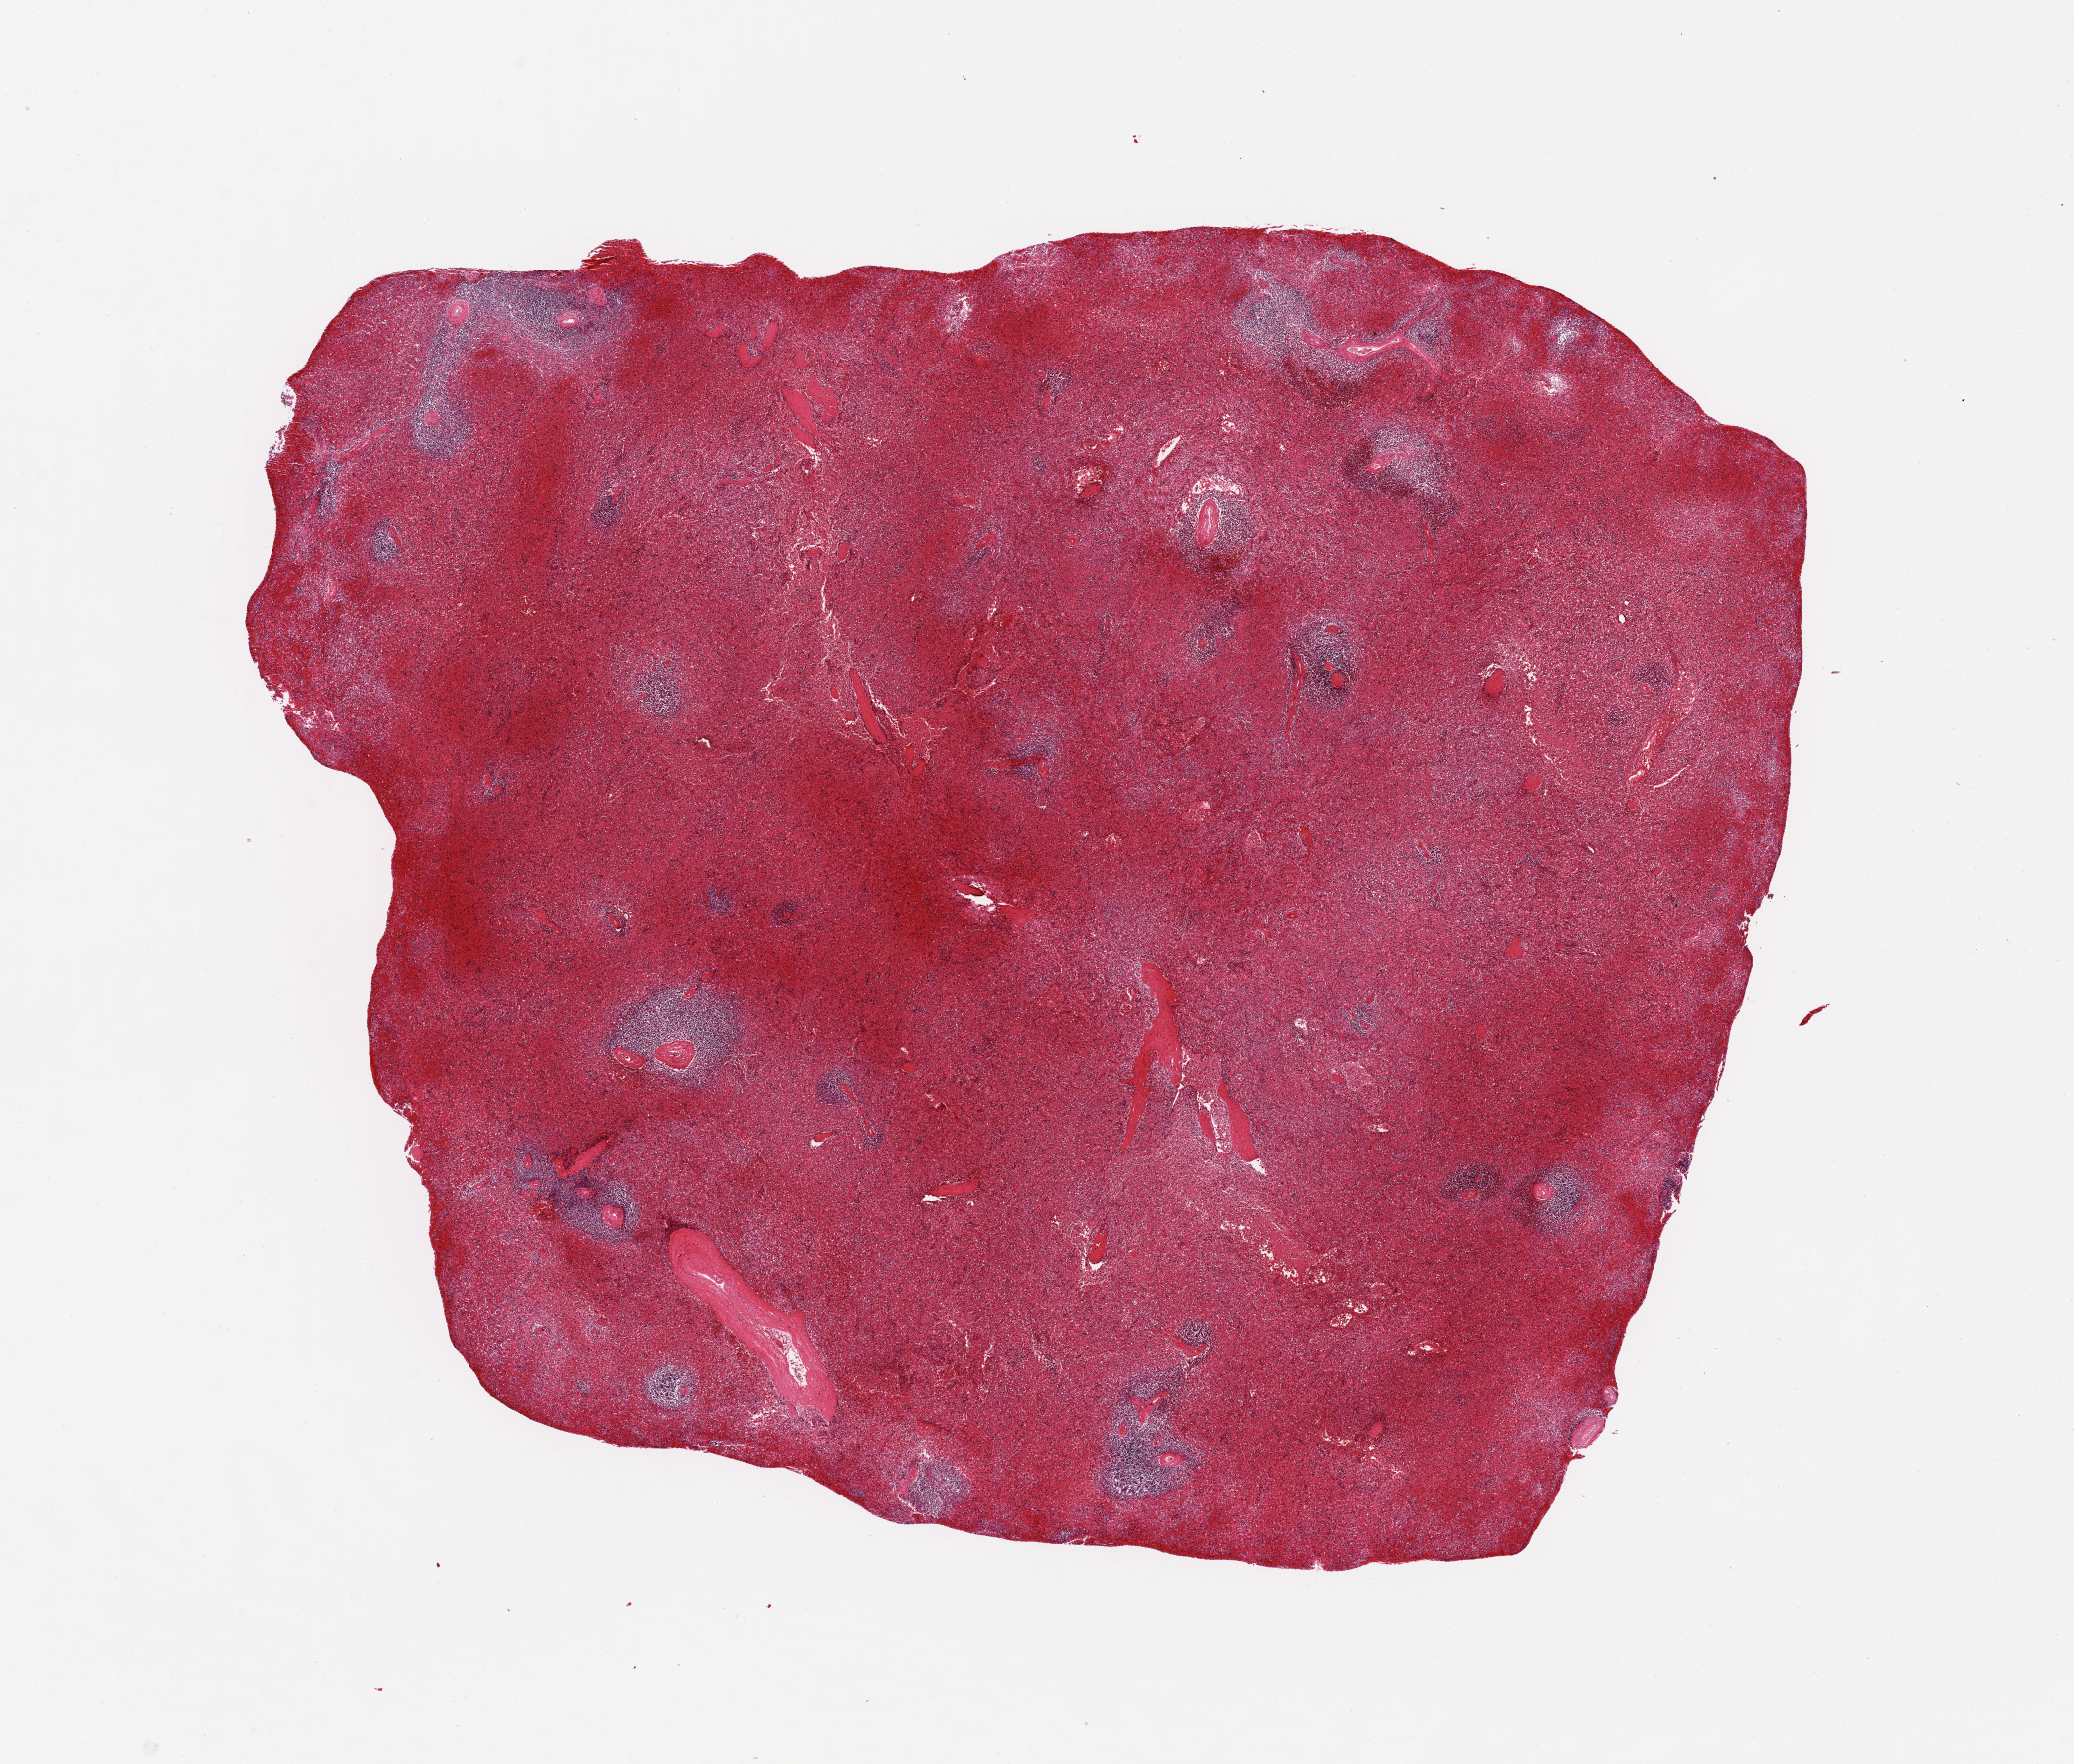
Haematoxylin and eosin whole-slide image, shown as a low-resolution overview of the whole scanned area (about 16.7 x 14.2 mm, acquisition: 20x scan); PAXgene-fixed, paraffin-embedded tissue; sampled site (target tissue): spleen; donor tissue sample. Male donor.
Reviewer comment on this tissue sample: Mild autolysis.